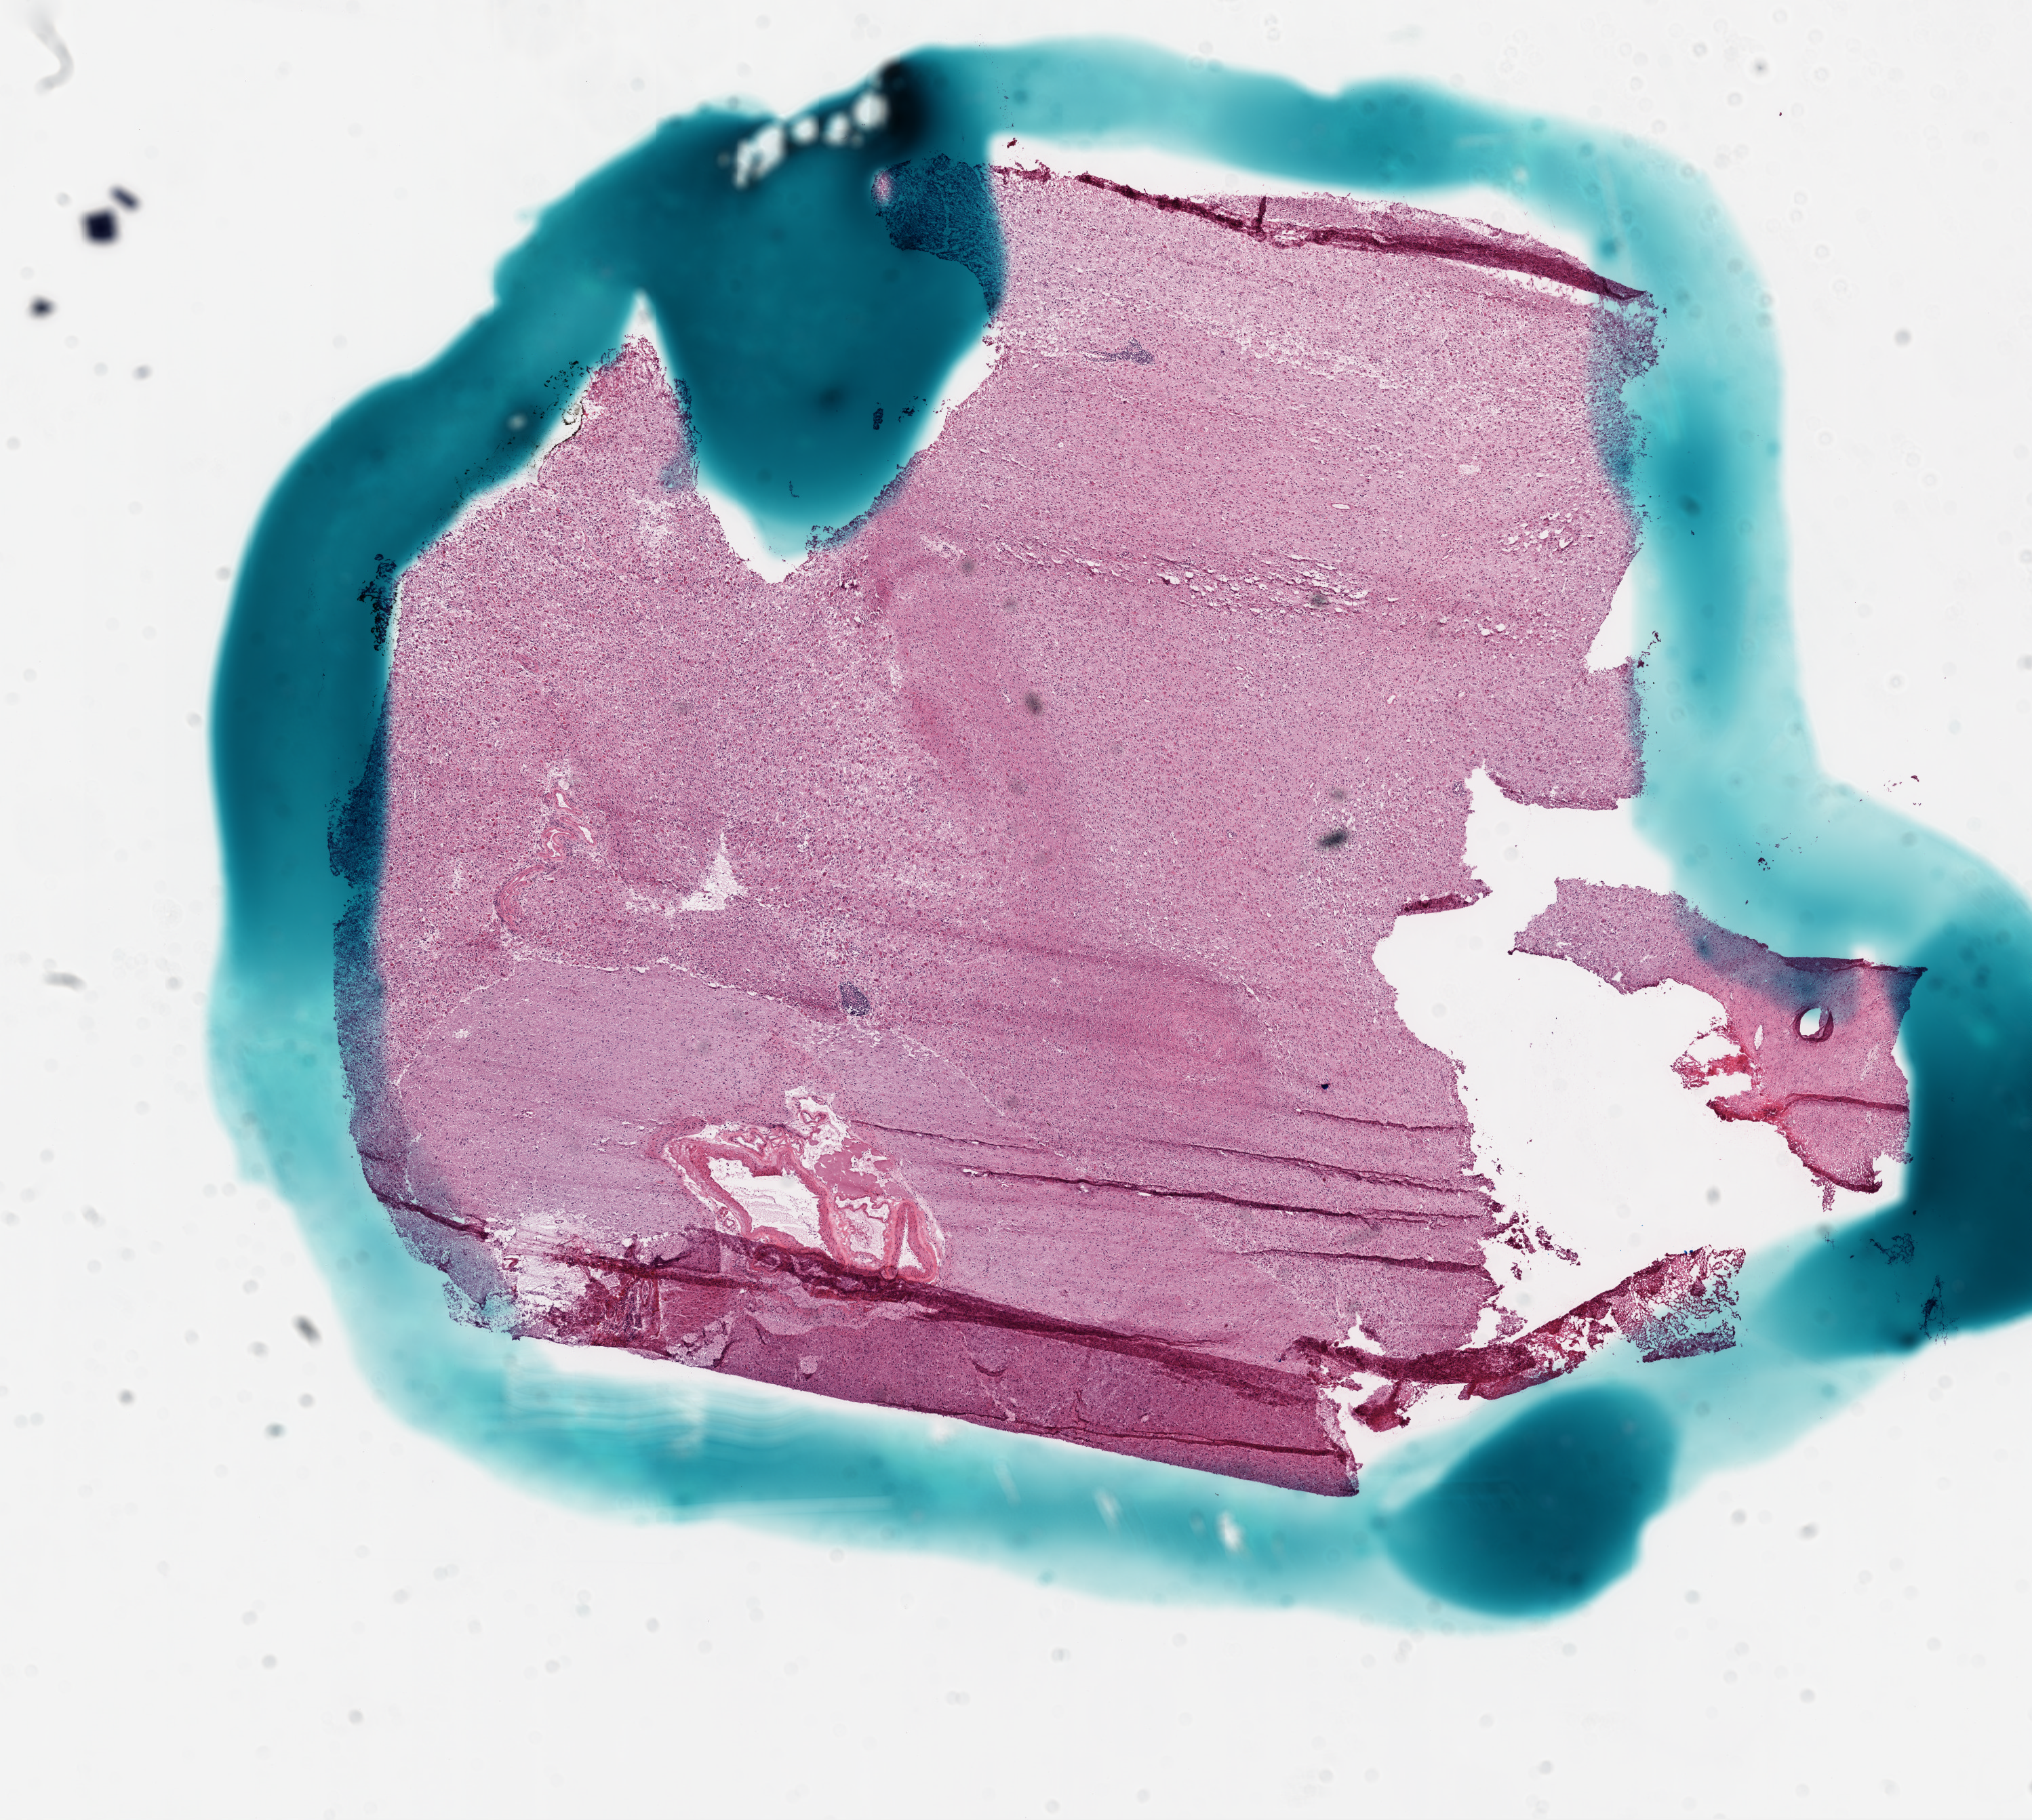
H&E-stained whole-slide image — shown as a low-resolution overview of the whole scanned area (about 12.1 x 10.8 mm, acquisition: 20x scan), frozen section from the bottom of the tissue portion, brain, primary tumour sample. Female patient; age at initial diagnosis 47 years. Composition of this section per pathologist review: tumour cells 80%, tumour nuclei 80%, normal cells 20%, stromal cells 0%, necrosis 0%. Infiltration values recorded for this section: lymphocyte infiltration 0%, monocyte infiltration 0%, neutrophil infiltration 0%.
Pathologic diagnosis: Glioblastoma.